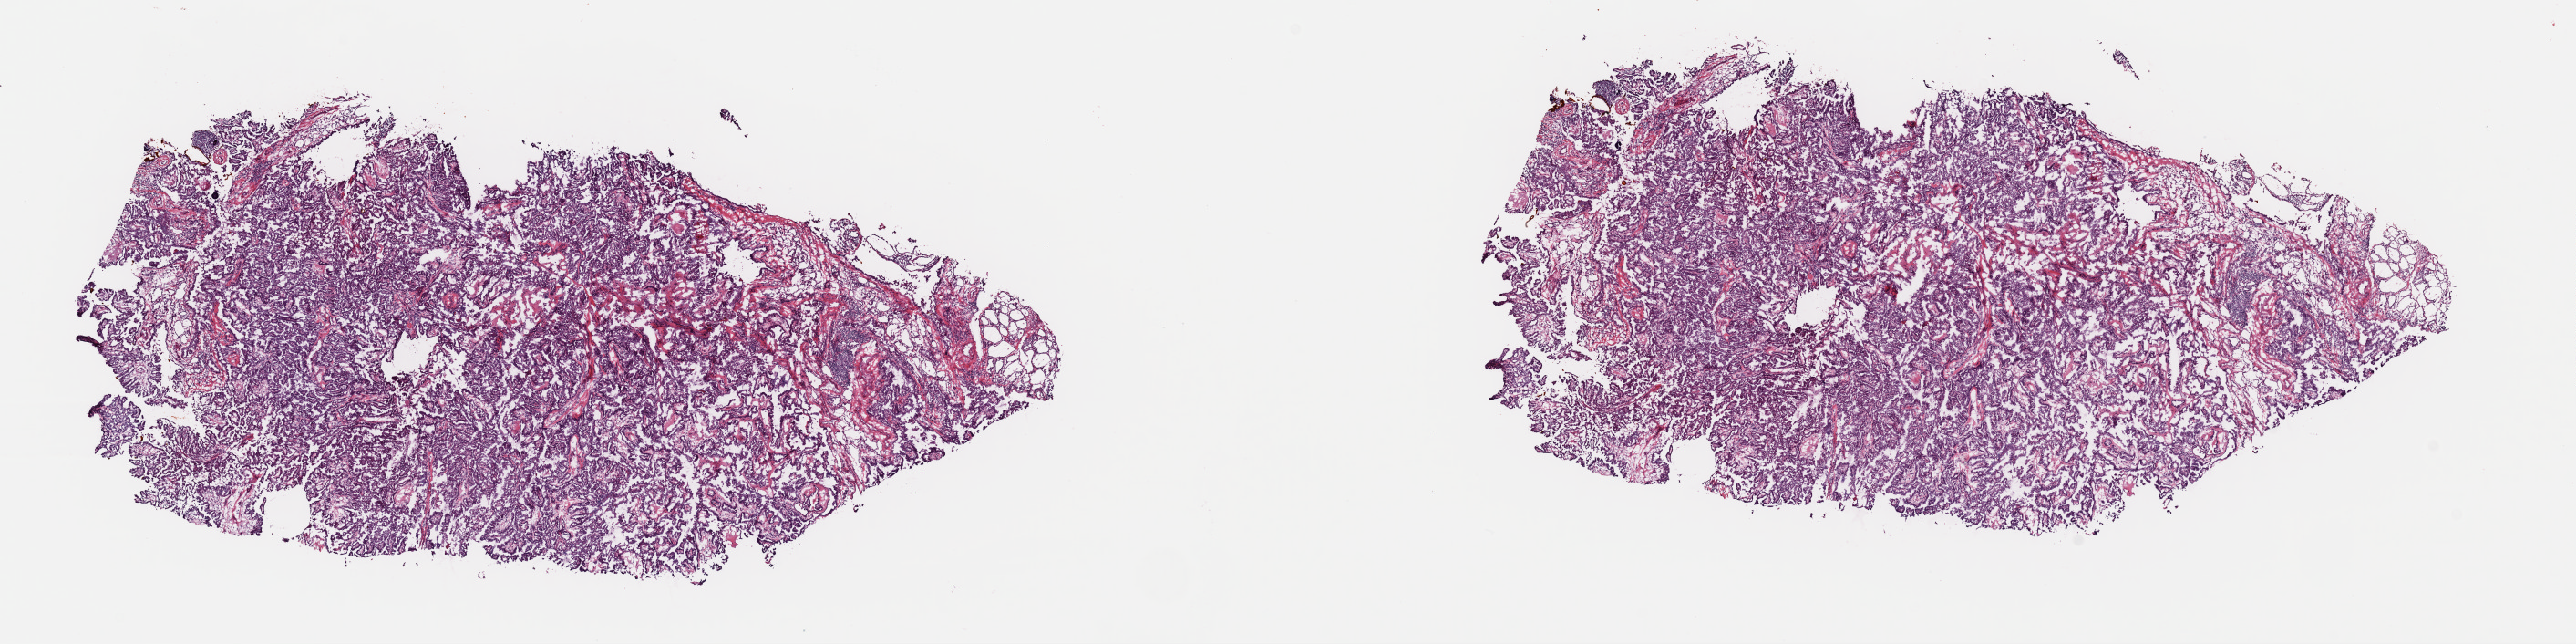
Digitized H&E tissue section (whole slide) — low-resolution overview of the scanned area, about 22.3 x 5.6 mm (acquisition: 40x scan); frozen section; primary tumour sample from the thyroid. Female, age 51 years at initial diagnosis. Pathologist review of this section (percent, as recorded): tumour cells 100%, tumour nuclei 95%, normal cells 0%, stromal cells 0%, necrosis 0%. Infiltration values recorded for this section: lymphocyte infiltration 0%, monocyte infiltration 0%, neutrophil infiltration 0%.
- AJCC pathologic stage: III (7th edition)
- pathologic diagnosis: Papillary adenocarcinoma, NOS (thyroid gland)
- laterality: right
- lymph nodes positive (case pathology): 20 of 27 examined